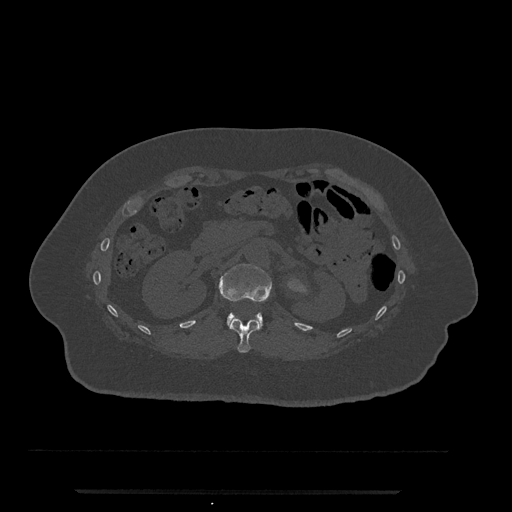
CT including the spine, one axial slice; bone window (W 1800 / L 400 HU); 0.5 mm slice thickness; 512 × 512 image matrix, field of view 440 × 440 mm. Female patient, age 51 years. Case-level facts recorded for this patient, not image findings: primary cancer: neuro; vertebrae with lytic lesions (as recorded): T8.
Outlined on this slice (semi-automatic segmentation, software-assisted and operator-edited):
- L1 vertebra: bounding box <219,264,272,329> (left, top, right, bottom; pixels)
- T12 vertebra: <229,317,259,353>